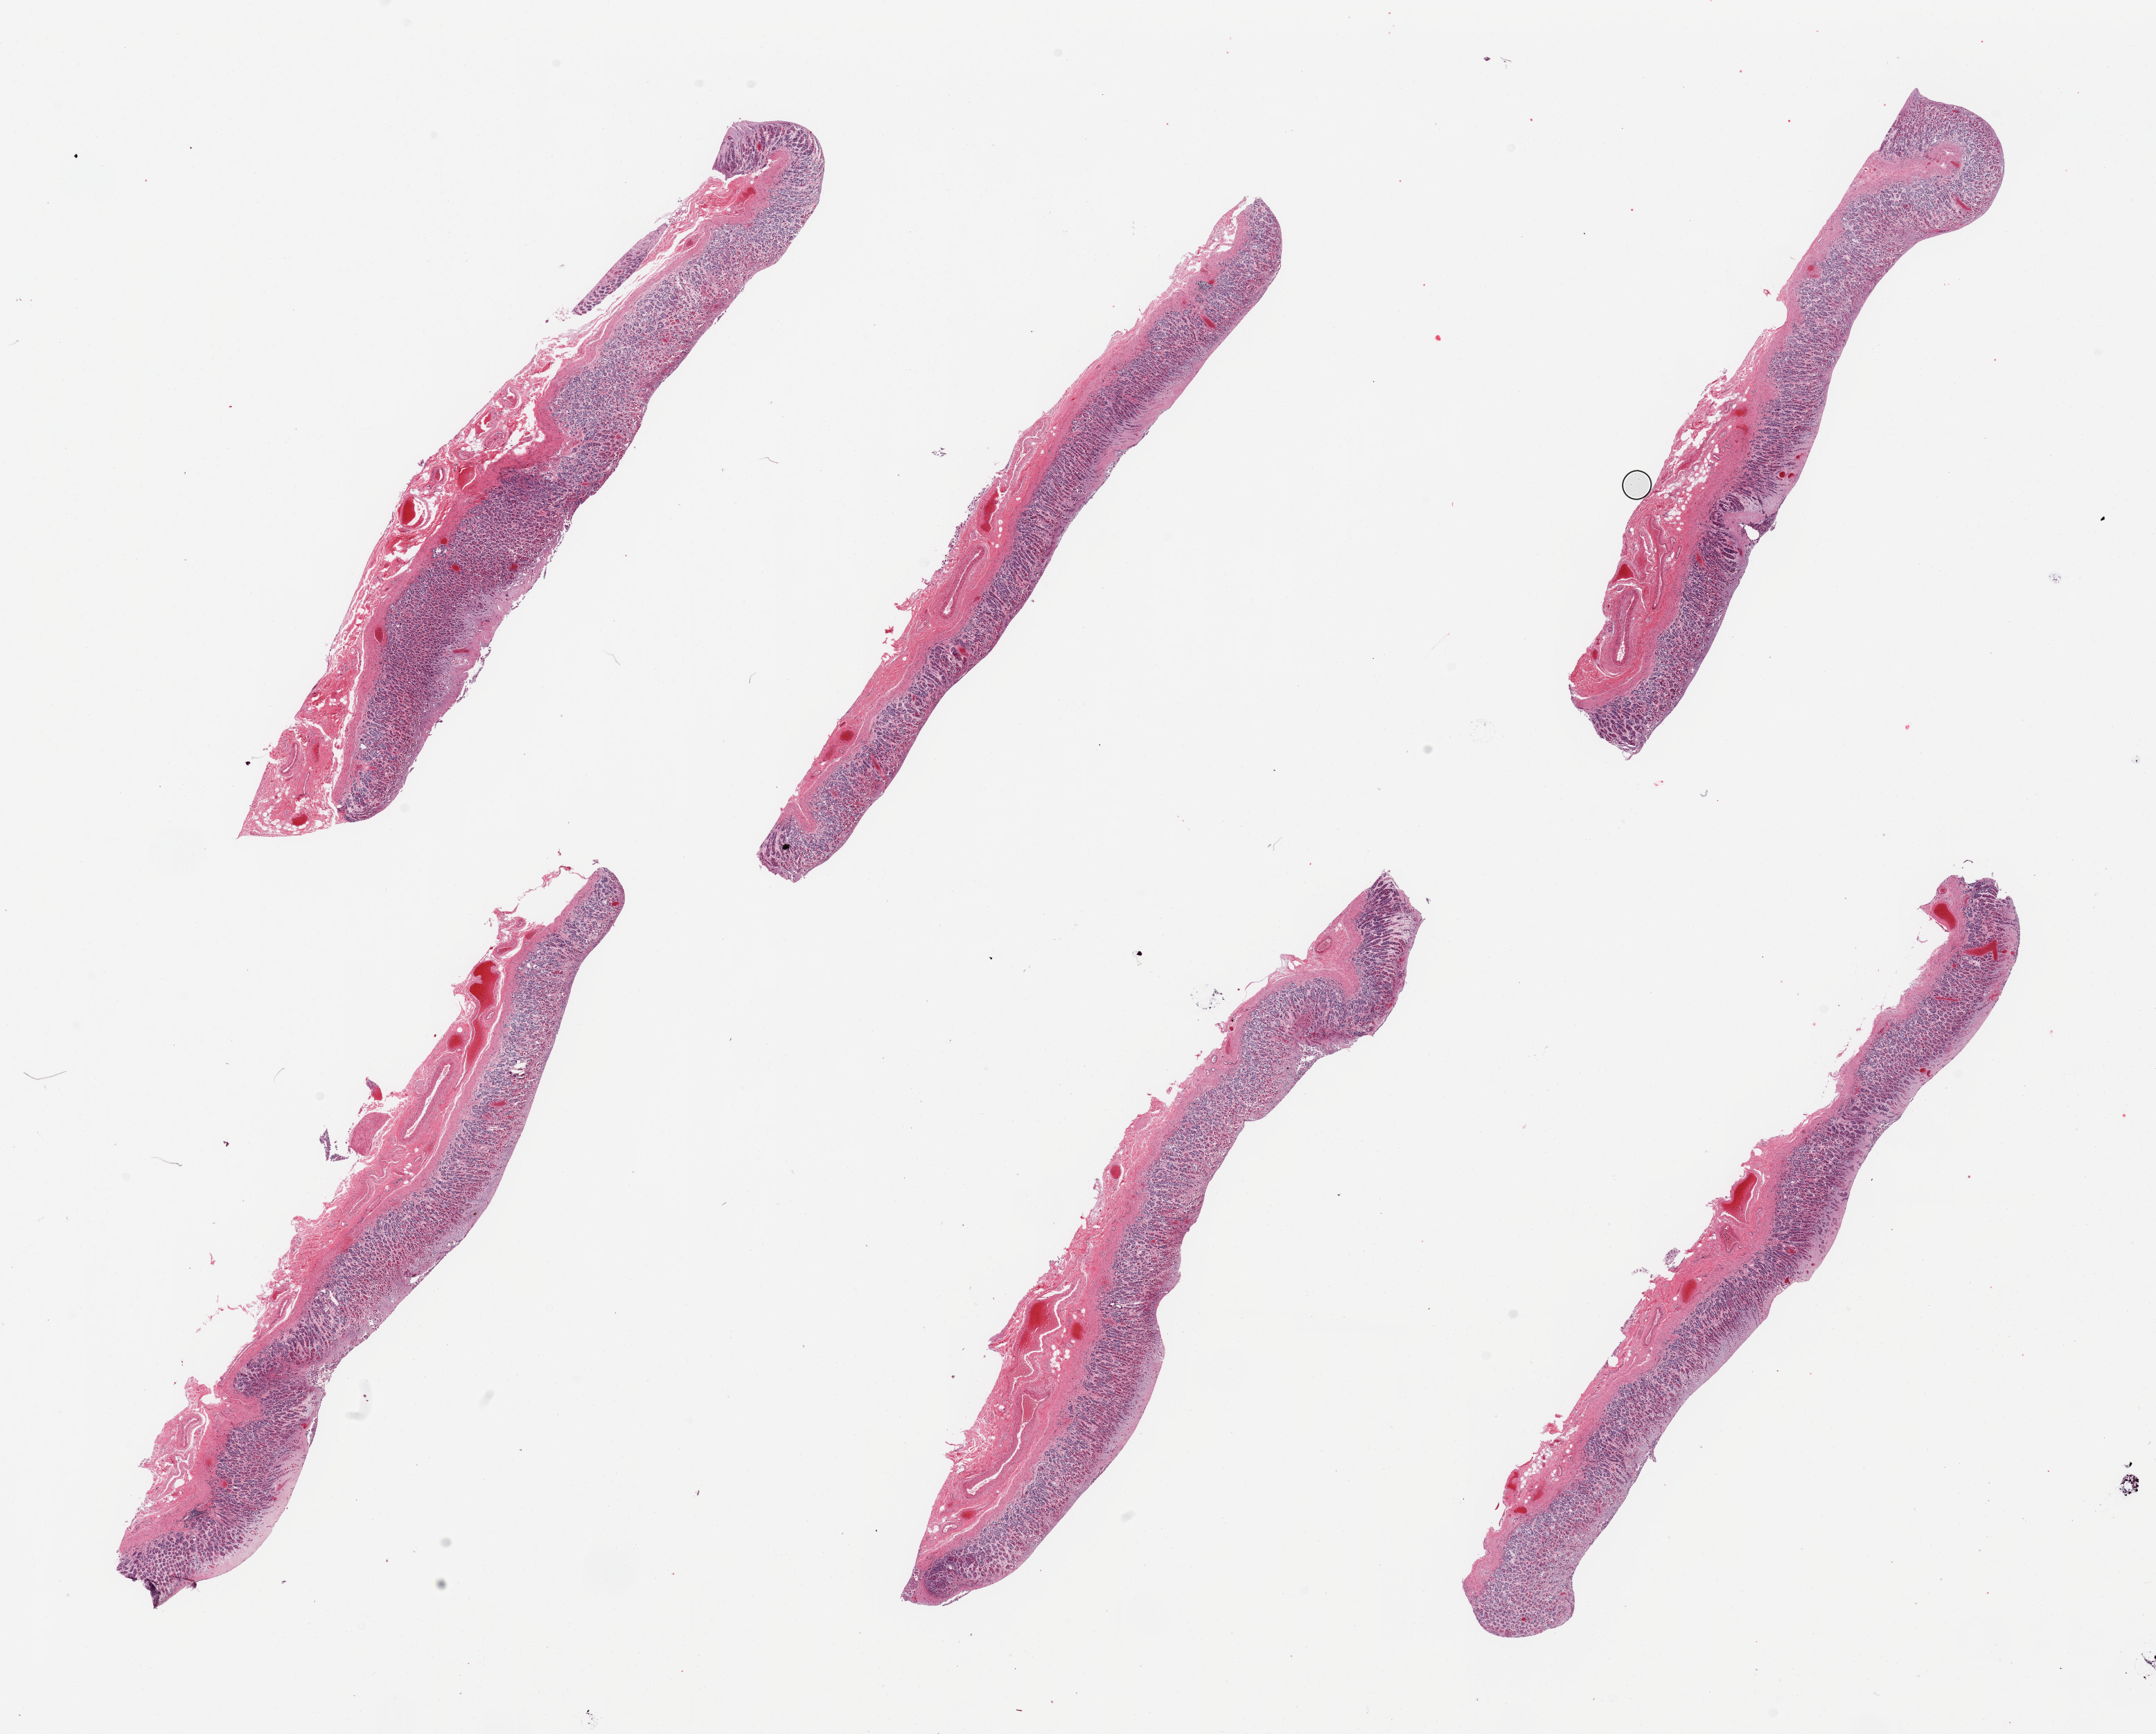
Hematoxylin and eosin (H&E) whole-slide image — a low-resolution overview of the entire scanned area, about 24.6 x 19.8 mm, PAXgene-fixed paraffin-embedded (PFPE) section, sampled site (target tissue): stomach, donor tissue sample. Male donor.
Reviewer comment on this tissue sample: 6 pieces, target mucosa up to ~0.8mm, moderate-advanced autolysis.